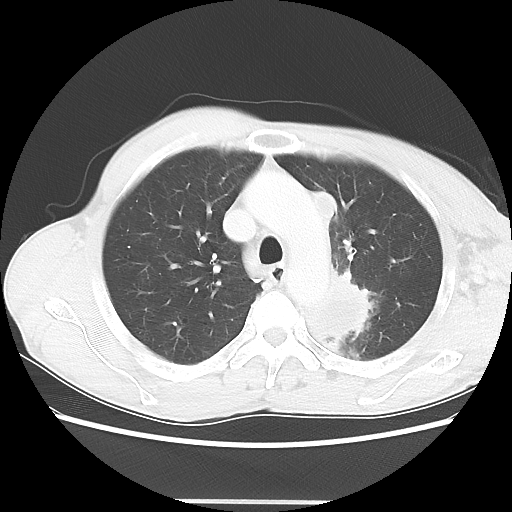
Chest CT, one axial slice. Position 48 of 62 along the scan axis. Lung window (W 1500 / L -600 HU). 512 × 512 image matrix, field of view 360 × 360 mm. Patient: male, 61 years. From the clinical record (not read from this slice): clinical TNM (as recorded): T3 N1 M1.
Annotated regions visible in this slice (bounding box drawn by a radiologist):
- lung tumour (recorded histology: adenocarcinoma): bounding box [x1, y1, x2, y2] px = [295, 255, 370, 348]
- lung tumour (recorded histology: adenocarcinoma): [309, 183, 342, 223]